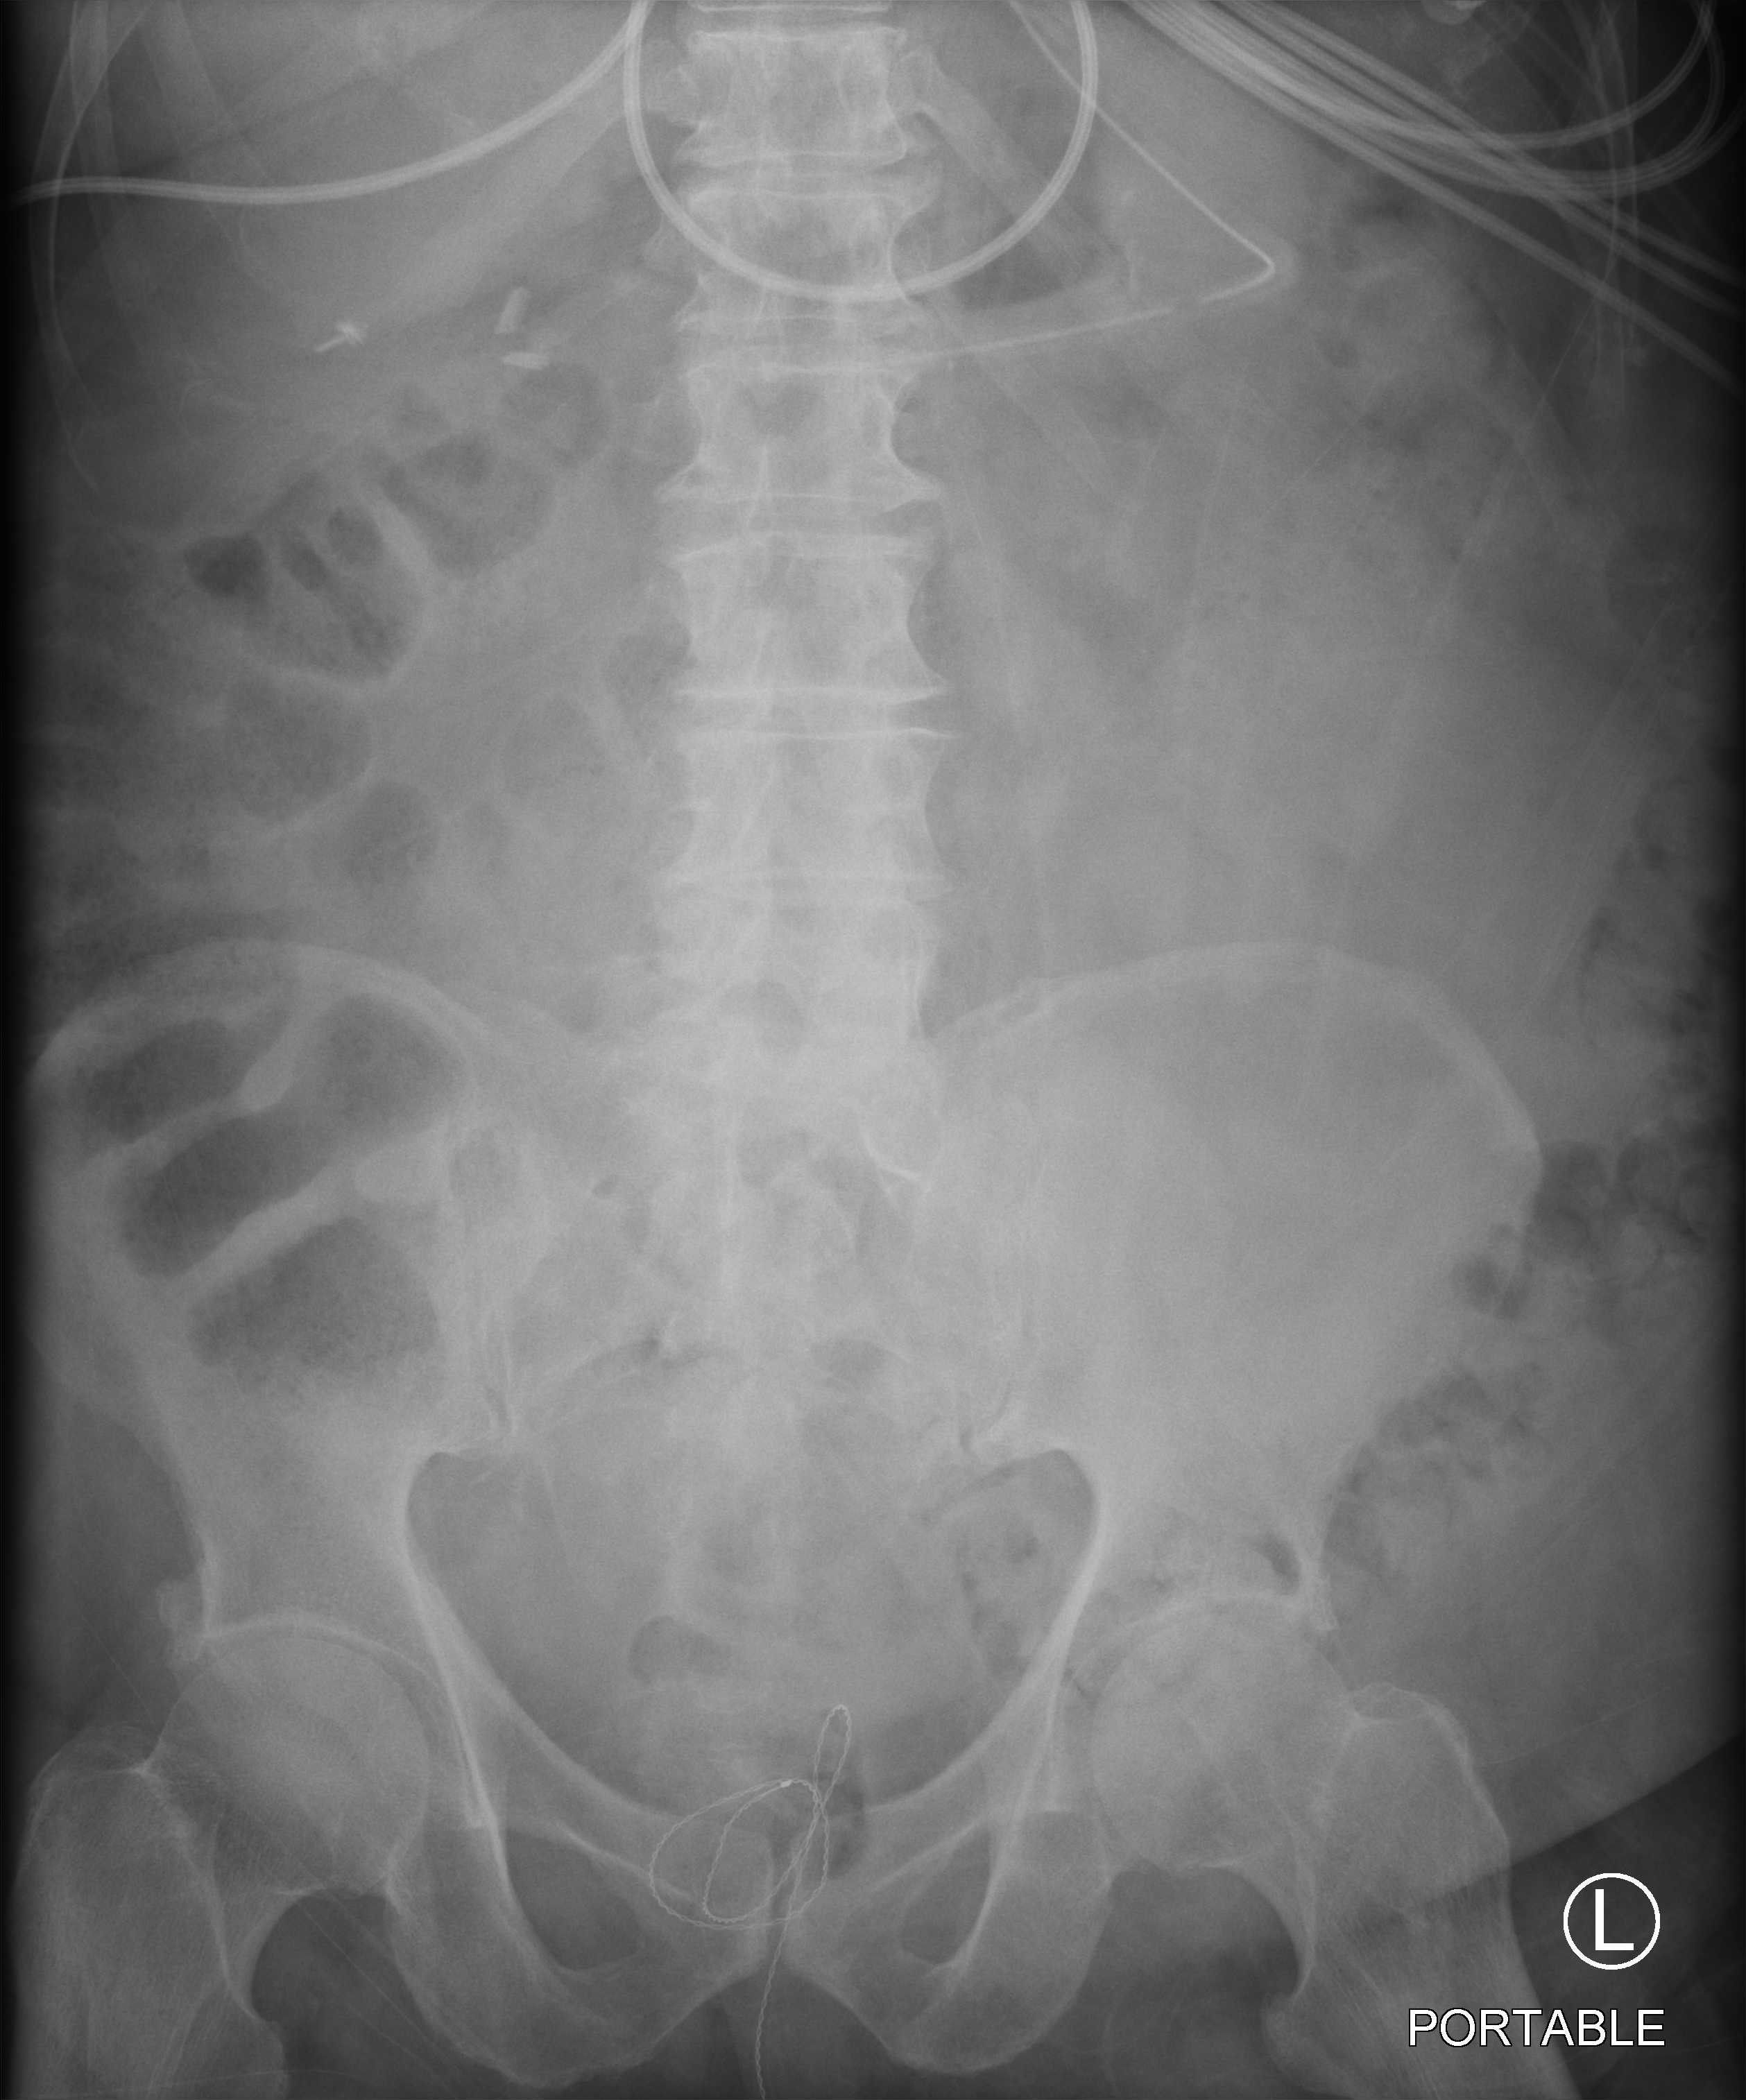
Abdomen X-ray (portable); anteroposterior (AP) projection. Patient hospitalised with COVID-19; male, aged 75–90 years.
From the hospital-stay record, not from the radiograph (when in the stay this image was taken is not recorded):
- mechanically ventilated during this hospital stay: yes
- smoking status (admission record): never